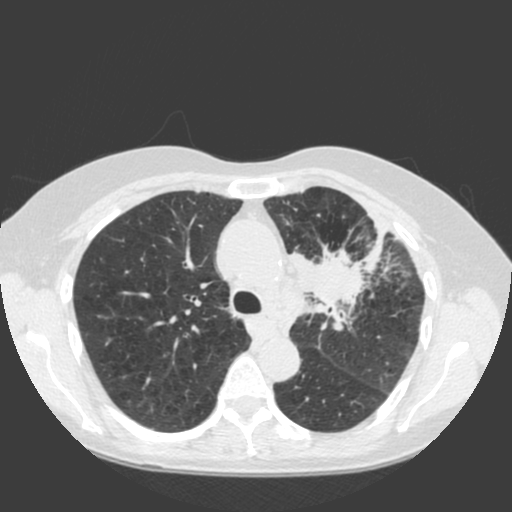
Low-dose screening chest CT, one axial slice. Position 132 of 184 along the scan axis. Lung window (W 1500 / L -600 HU). 2 mm slice thickness. 512 × 512 image matrix.
Annotated regions visible in this slice (manually delineated by an expert):
- lesion 1 (tumor, hilum of left lung): bounding box (x1, y1, x2, y2) in pixels: (289, 218, 388, 331)